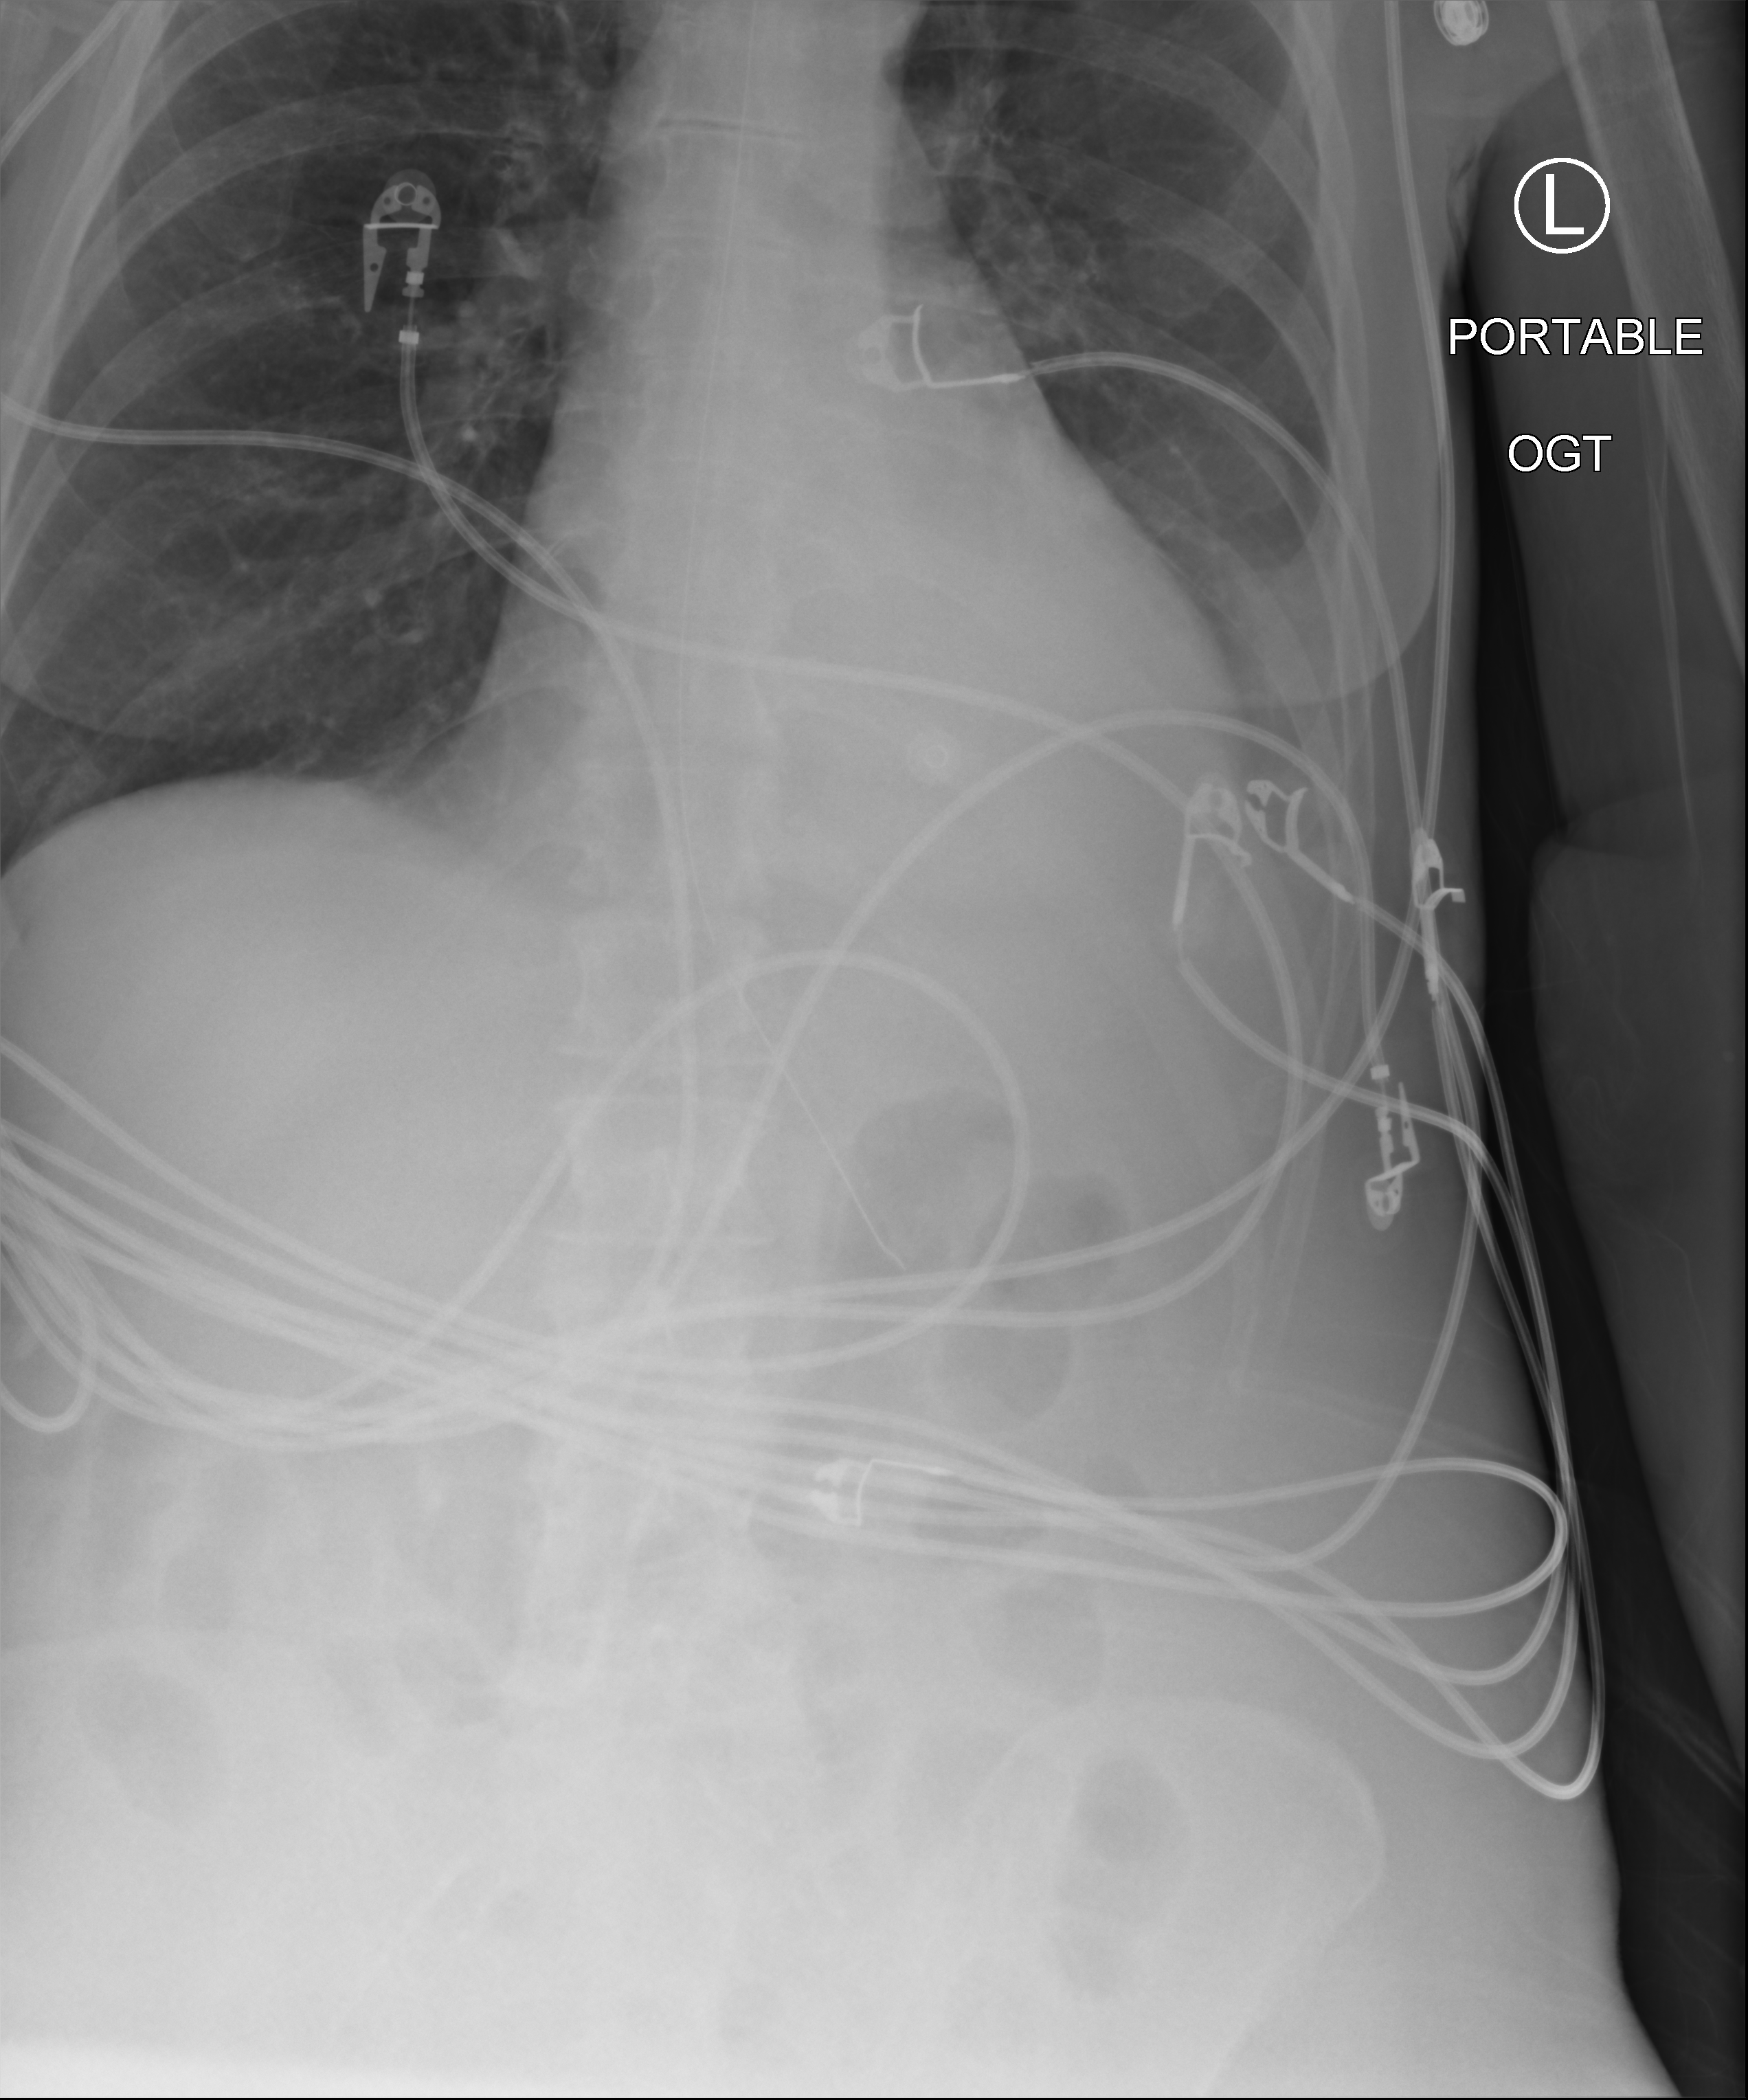
Portable chest radiograph, anteroposterior (AP) projection. Patient hospitalised with COVID-19; female, aged 60–74 years.
Hospital-stay facts (about this admission, not read from this image; timing relative to this image not recorded): mechanically ventilated during this hospital stay: yes; admitted to intensive care during this hospital stay: yes.